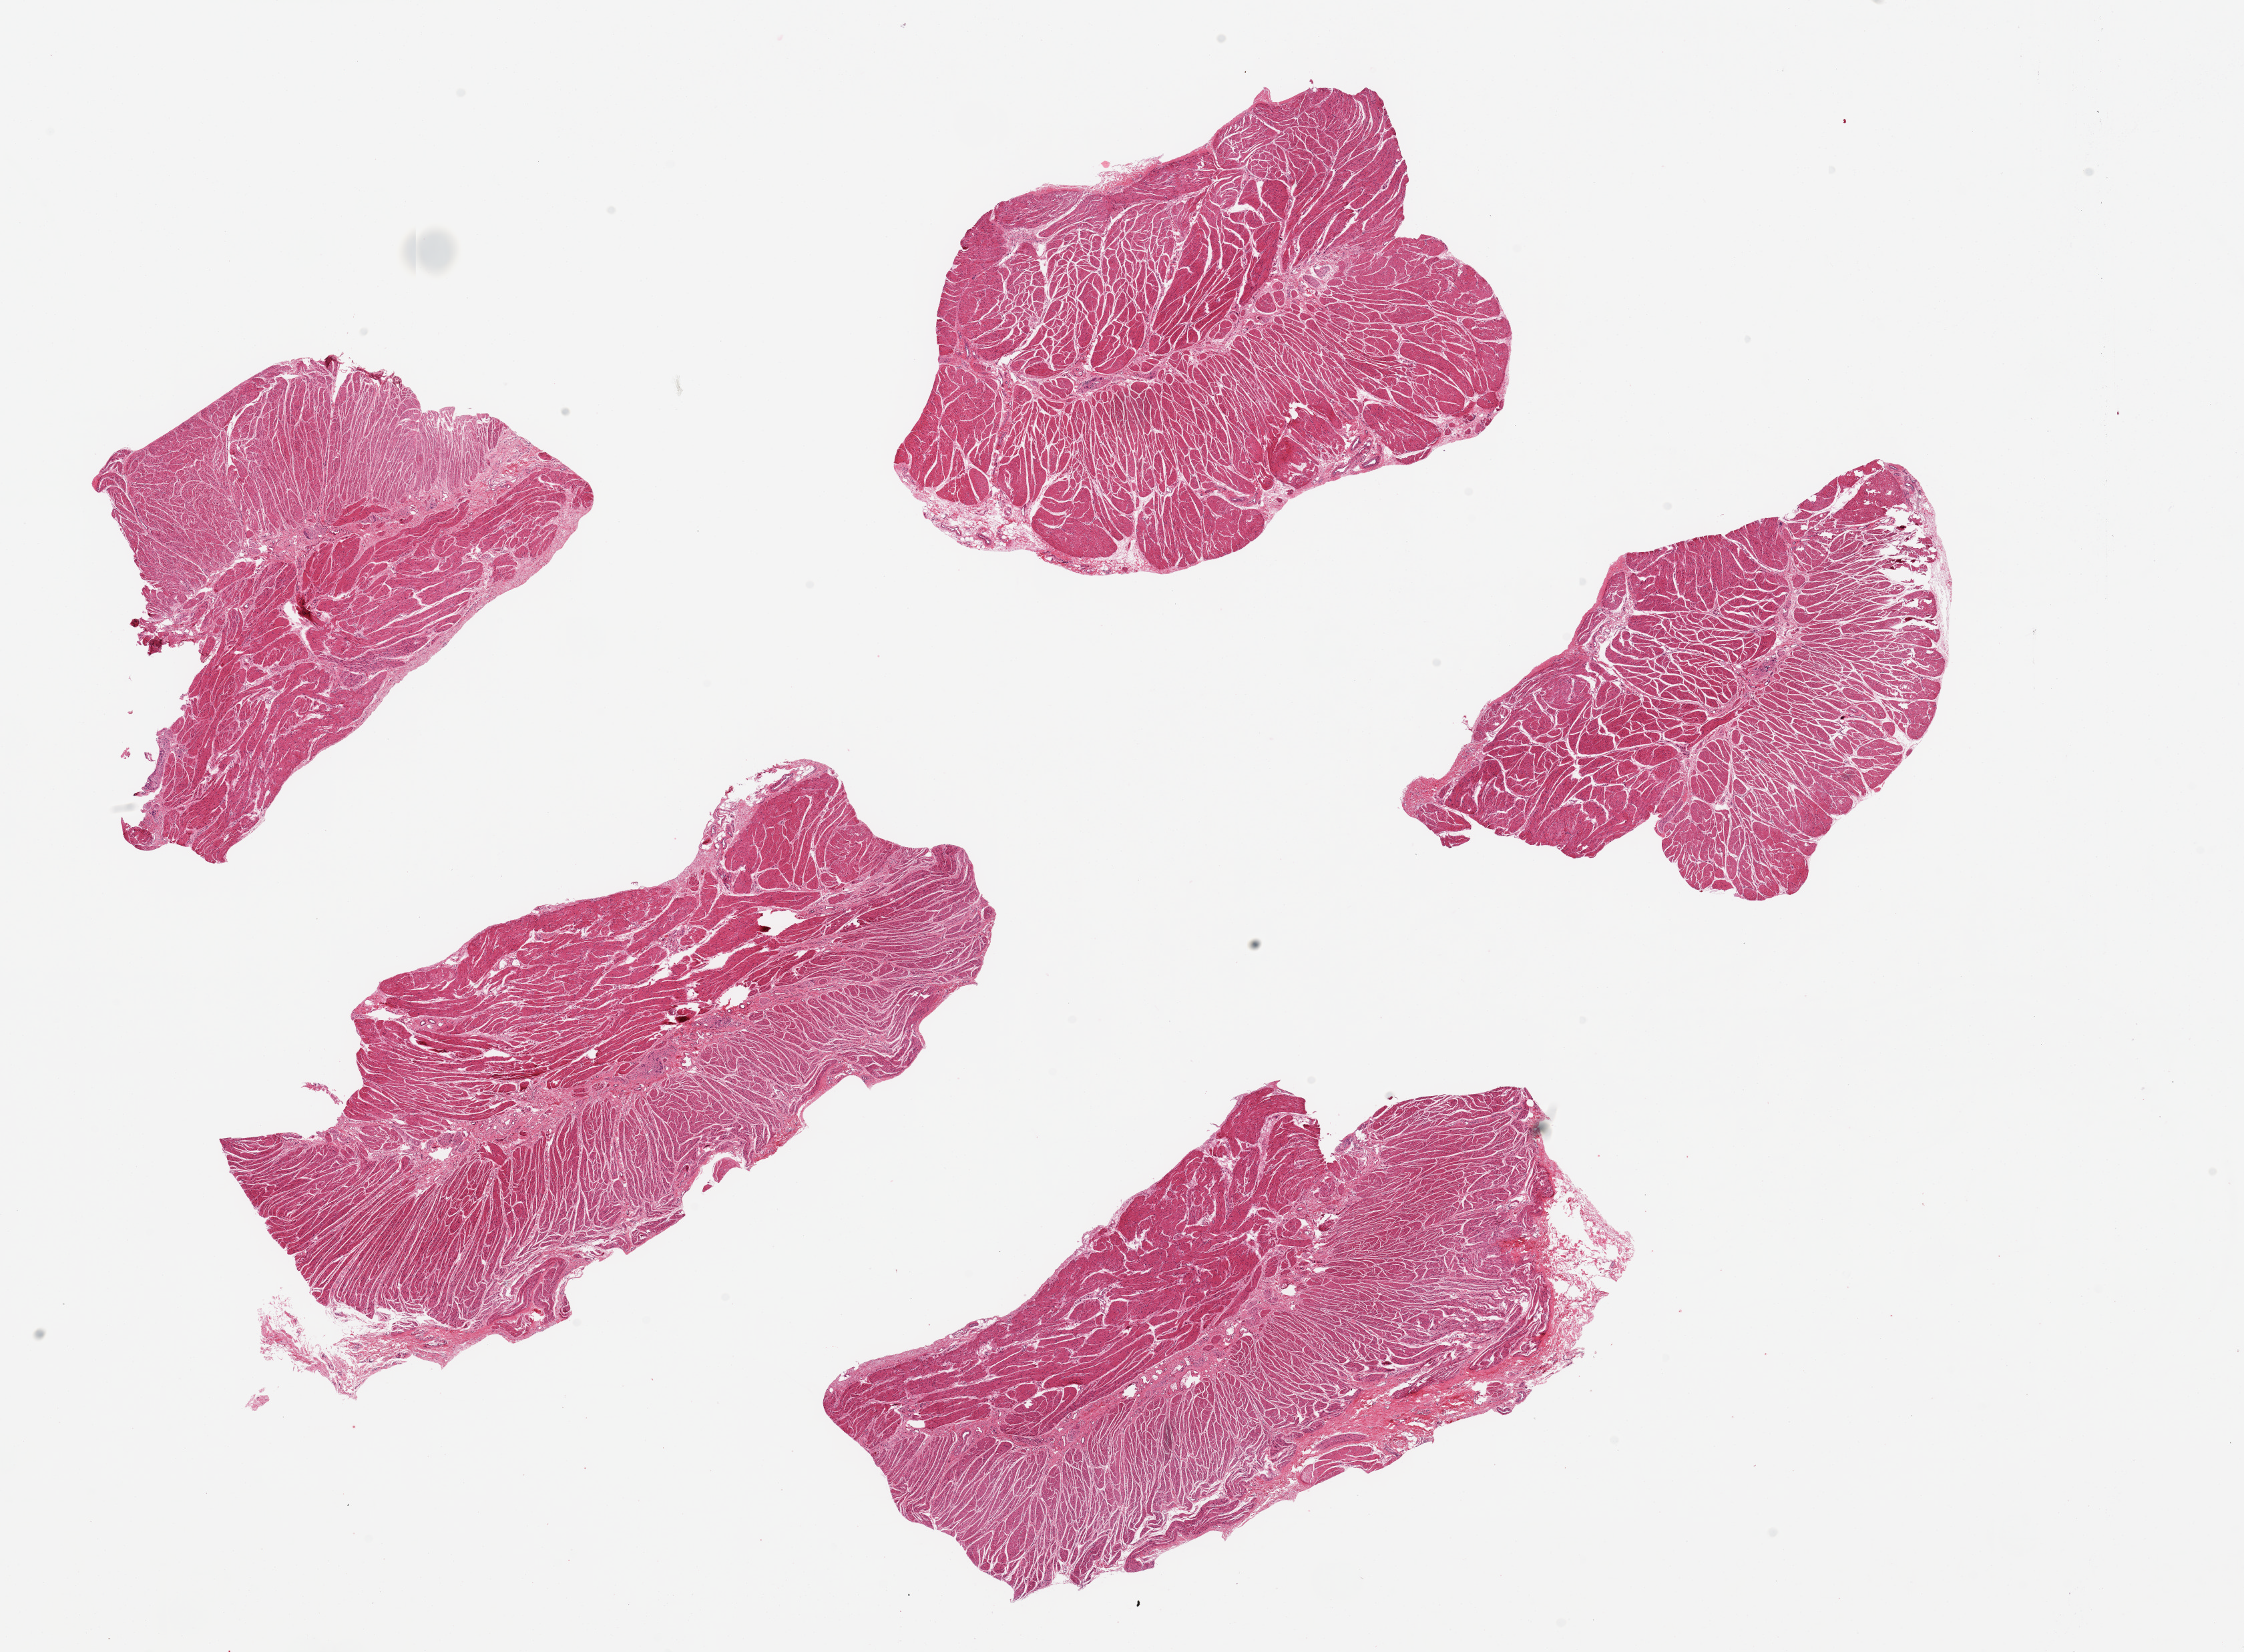
Digitized hematoxylin and eosin (H&E)-stained section, brightfield, low-resolution overview of the scanned area, about 26.6 x 19.6 mm, PAXgene-fixed paraffin-embedded (PFPE) section, section of esophageal muscle (target tissue), tissue donor sample. Male donor.
- review note (as recorded): 5 pieces, ~9x4.5 mm. well-oriented specimens